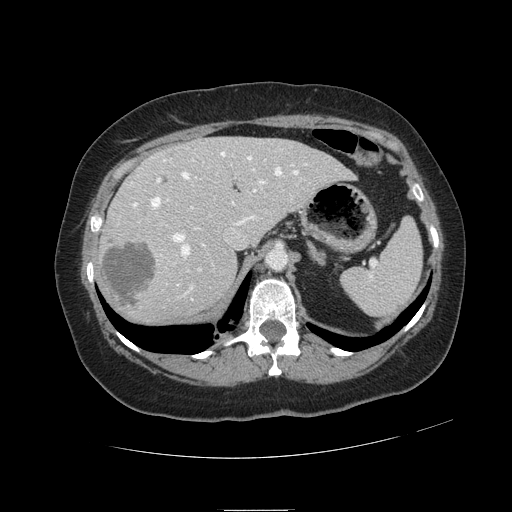
Contrast-enhanced abdominal CT, one axial slice; position 79 of 121 along the scan axis; 120 kVp; soft-tissue window (W 400 / L 40 HU); 512 × 512 image matrix, field of view 400 × 400 mm. Female patient, age 52 years. From the clinical record (not read from this slice): diagnosis: colorectal cancer liver metastases, imaged before liver resection; multiple liver metastases: yes; largest metastasis: 6.3 cm; disease in both lobes: no.
Outlined on this slice (manually delineated by an expert):
- hepatic veins: bounding box <133,152,307,300> (left, top, right, bottom; pixels)
- liver: <100,137,350,322>
- planned liver remnant (the part of the liver to remain after resection): <168,137,350,239>
- portal vein (with intrahepatic branches): <157,160,266,296>
- liver metastasis: <101,238,157,307>